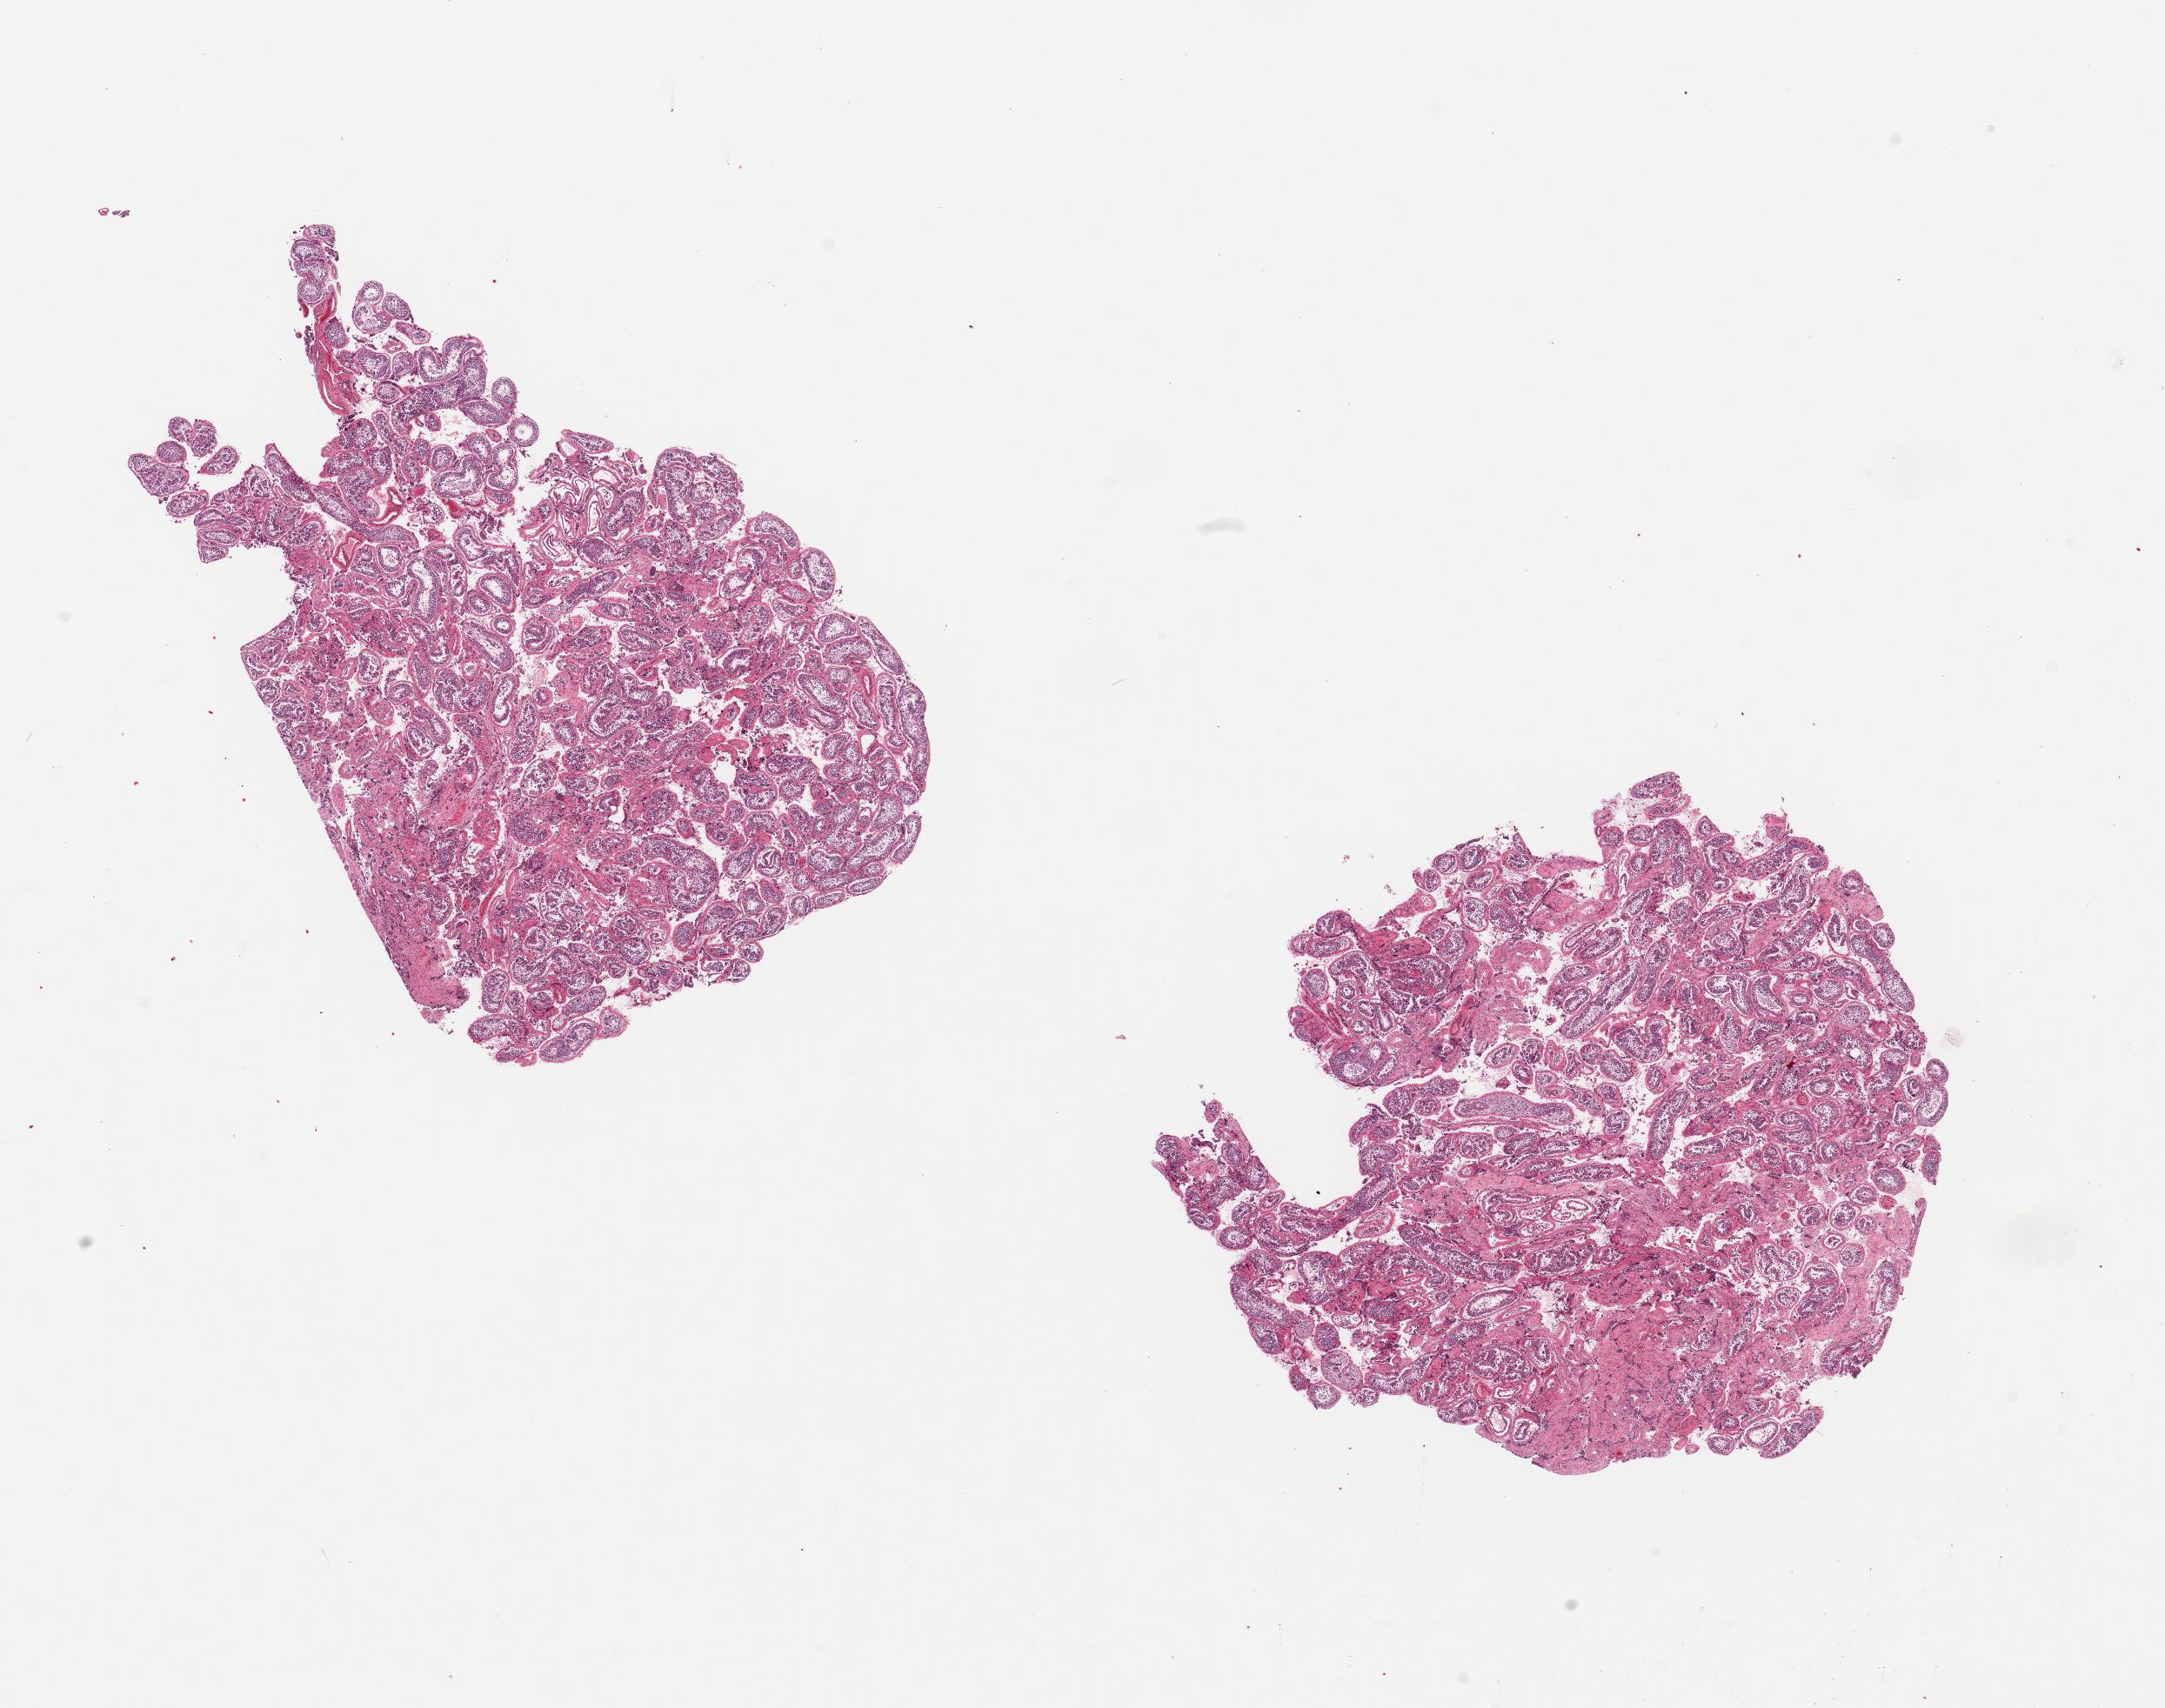
Hematoxylin and eosin (H&E) whole-slide image — shown as a low-resolution overview of the whole scanned area (about 19.7 x 15.5 mm), PAXgene-fixed paraffin-embedded (PFPE) section, section of testis (target tissue), tissue donor sample. Donor sex: male.
Reviewer comment on this tissue sample: 2 pieces ~6x6mm. Spermatogenesis is present but poorly preserved.